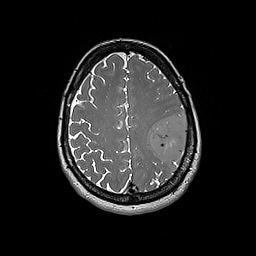
Brain MRI from a brain-tumour surgery series, one axial slice. Position 64 of 192 along the scan axis. 256 × 256 image matrix. Case-level facts recorded for this patient, not image findings: histopathology: Glioblastoma; WHO grade: 4; IDH mutation: no.
Outlined on this slice (expert manual segmentation):
- tumour: bounding box (x1, y1, x2, y2) in pixels: (149, 114, 188, 163)